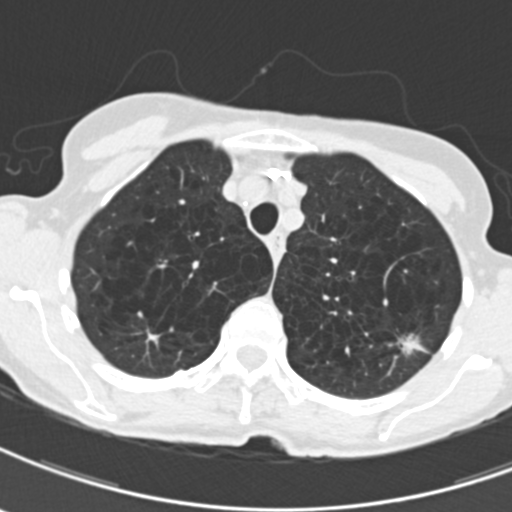
Low-dose screening chest CT, one axial slice; slice 159 of 203 in the series (ordered by position); 120 kVp; lung window (W 1500 / L -600 HU); 2 mm slice thickness; 512 × 512 image matrix, field of view 279 × 279 mm.
Annotated regions visible in this slice (expert manual segmentation):
- lesion 1 (tumor, upper lobe of left lung): bounding box [x1, y1, x2, y2] px = [398, 333, 426, 359]